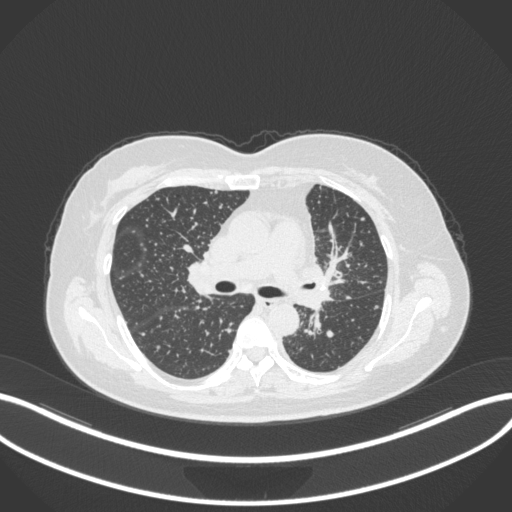
Chest CT, one axial slice; slice 203 of 348 in the series (ordered by position); reconstruction kernel B31f; 120 kVp; lung window (W 1500 / L -600 HU); 512 × 512 image matrix, field of view 400 × 400 mm. Patient: female, 49 years. Case-level facts recorded for this patient, not image findings: clinical TNM (as recorded): T1c N0 M1.
Annotated regions visible in this slice (bounding box drawn by a radiologist):
- lung tumour (recorded histology: adenocarcinoma): box from (x=294, y=253) to (x=337, y=314) px